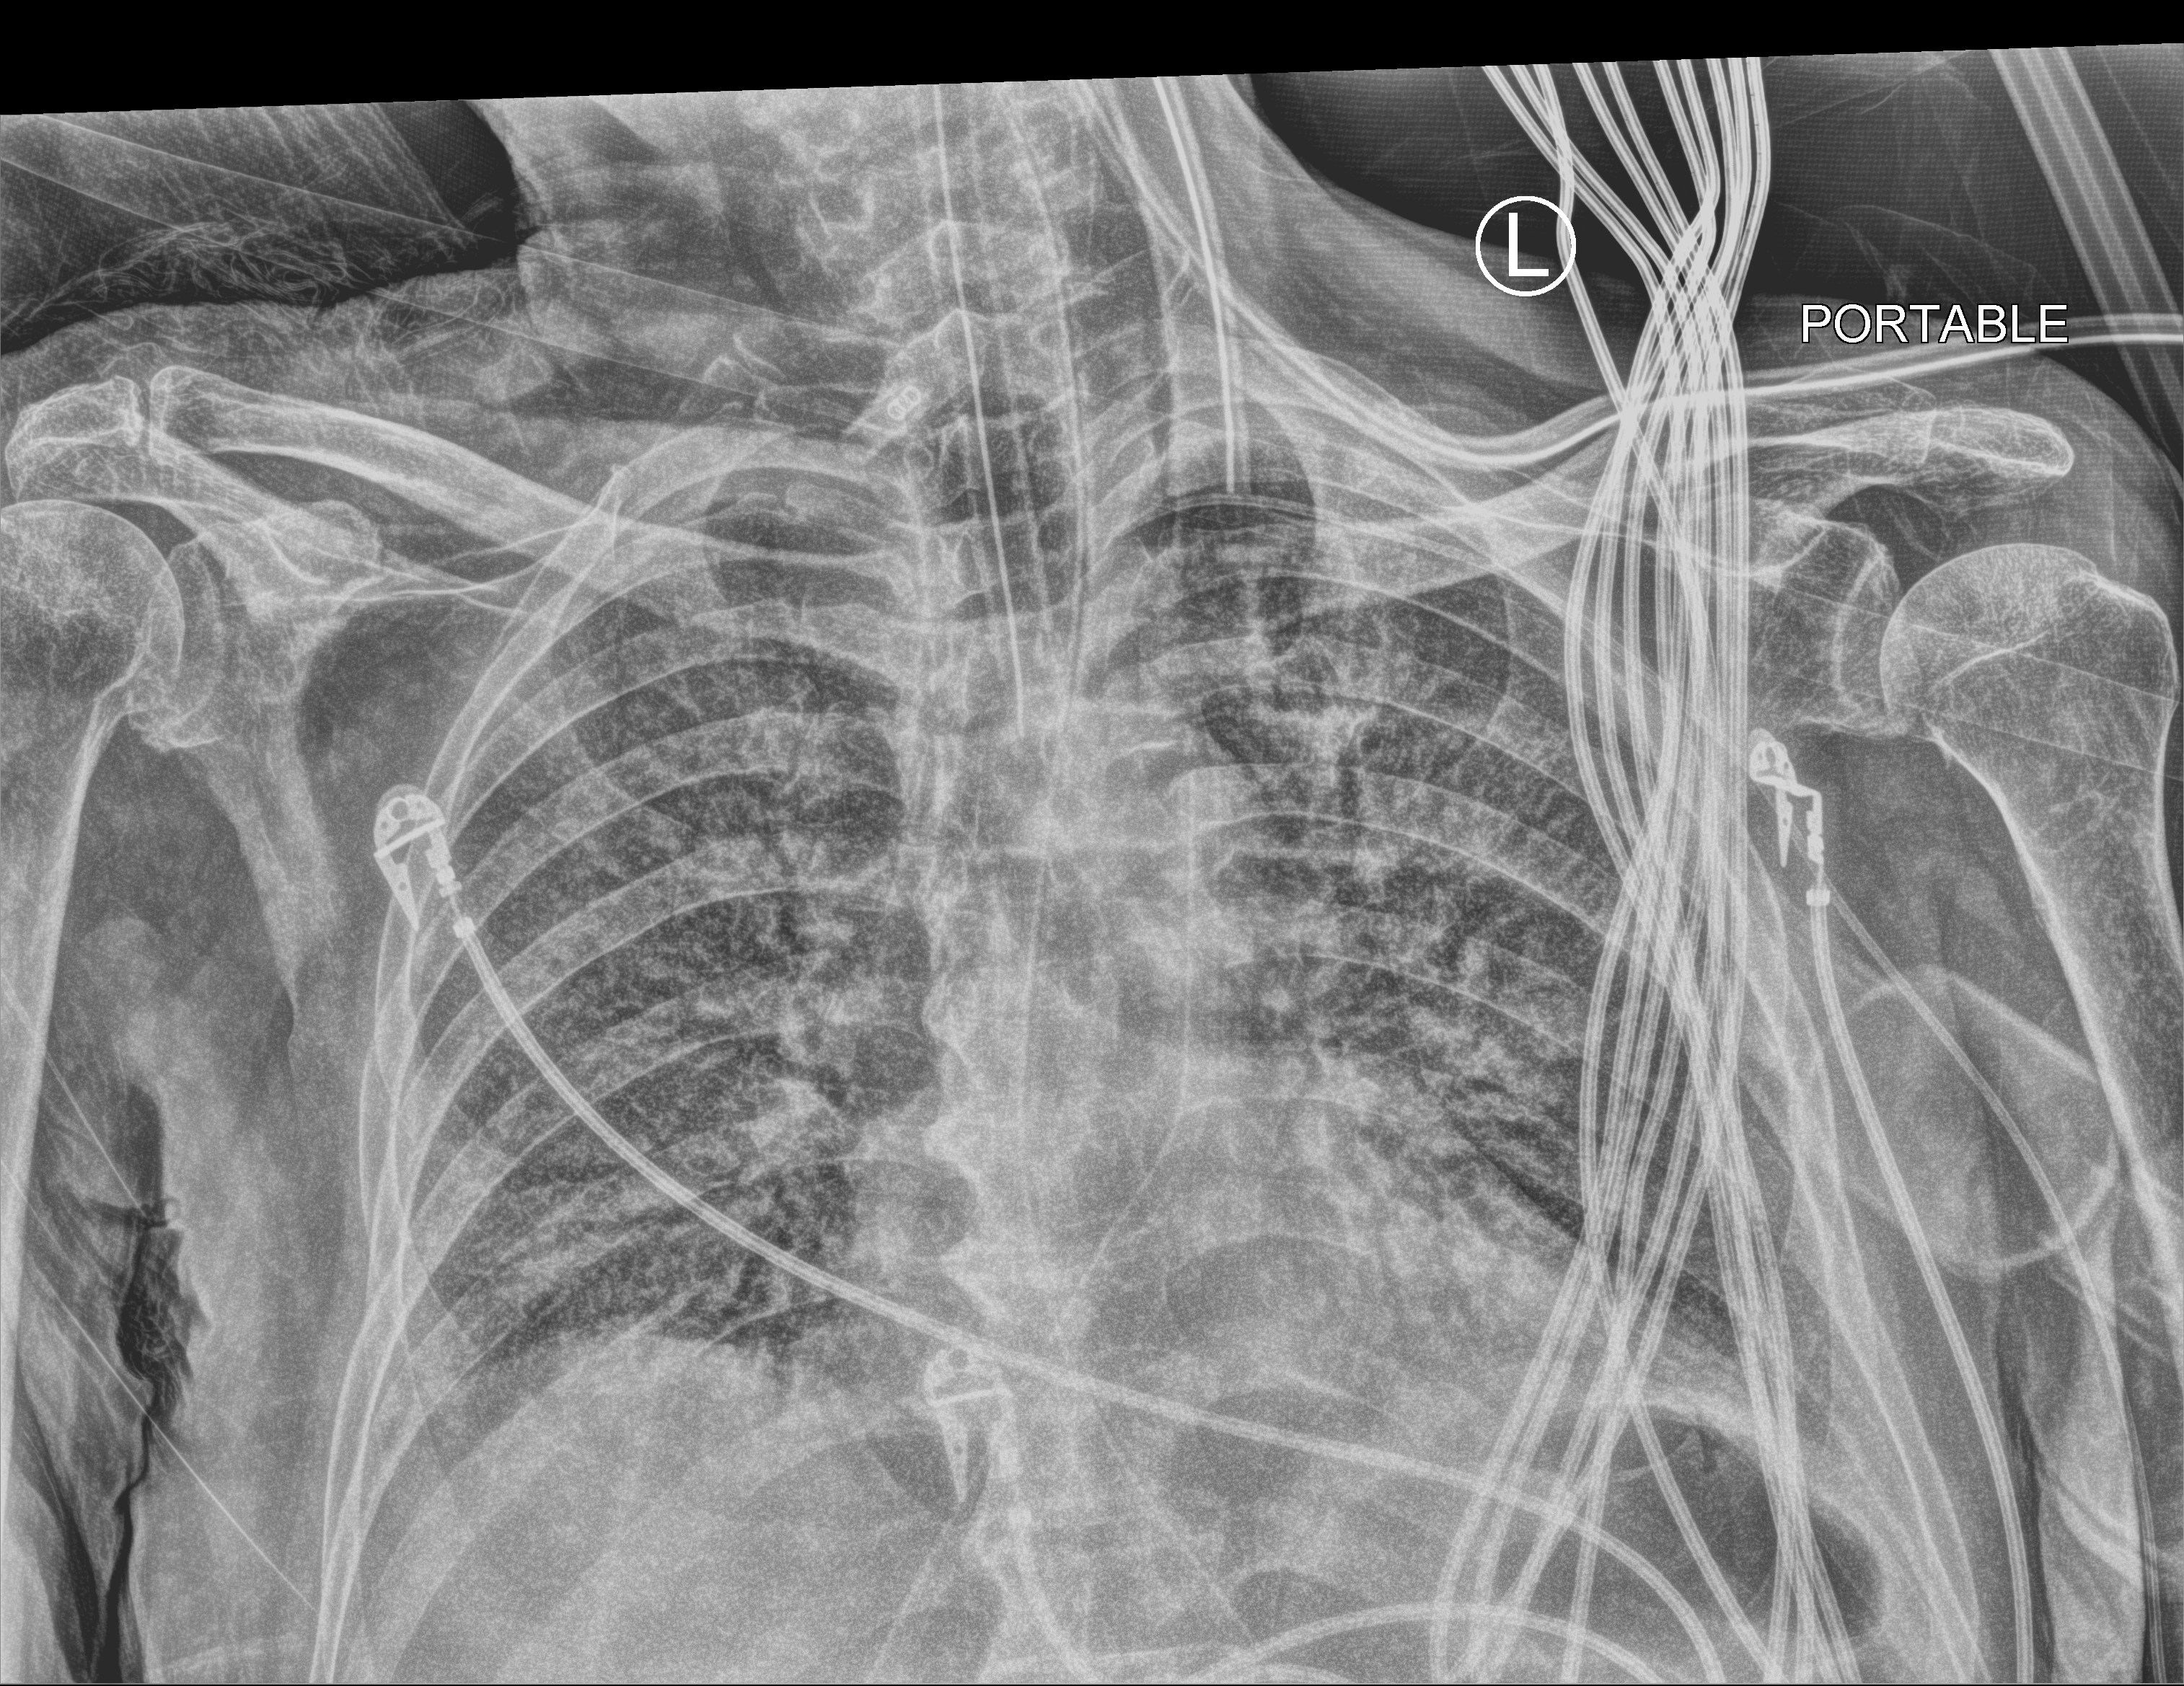
Portable chest radiograph. Male patient hospitalised with COVID-19, age 75–90 years.
From the hospital-stay record, not from the radiograph (when in the stay this image was taken is not recorded): mechanically ventilated during this hospital stay: yes; smoking status (admission record): never; admitted to intensive care during this hospital stay: yes.